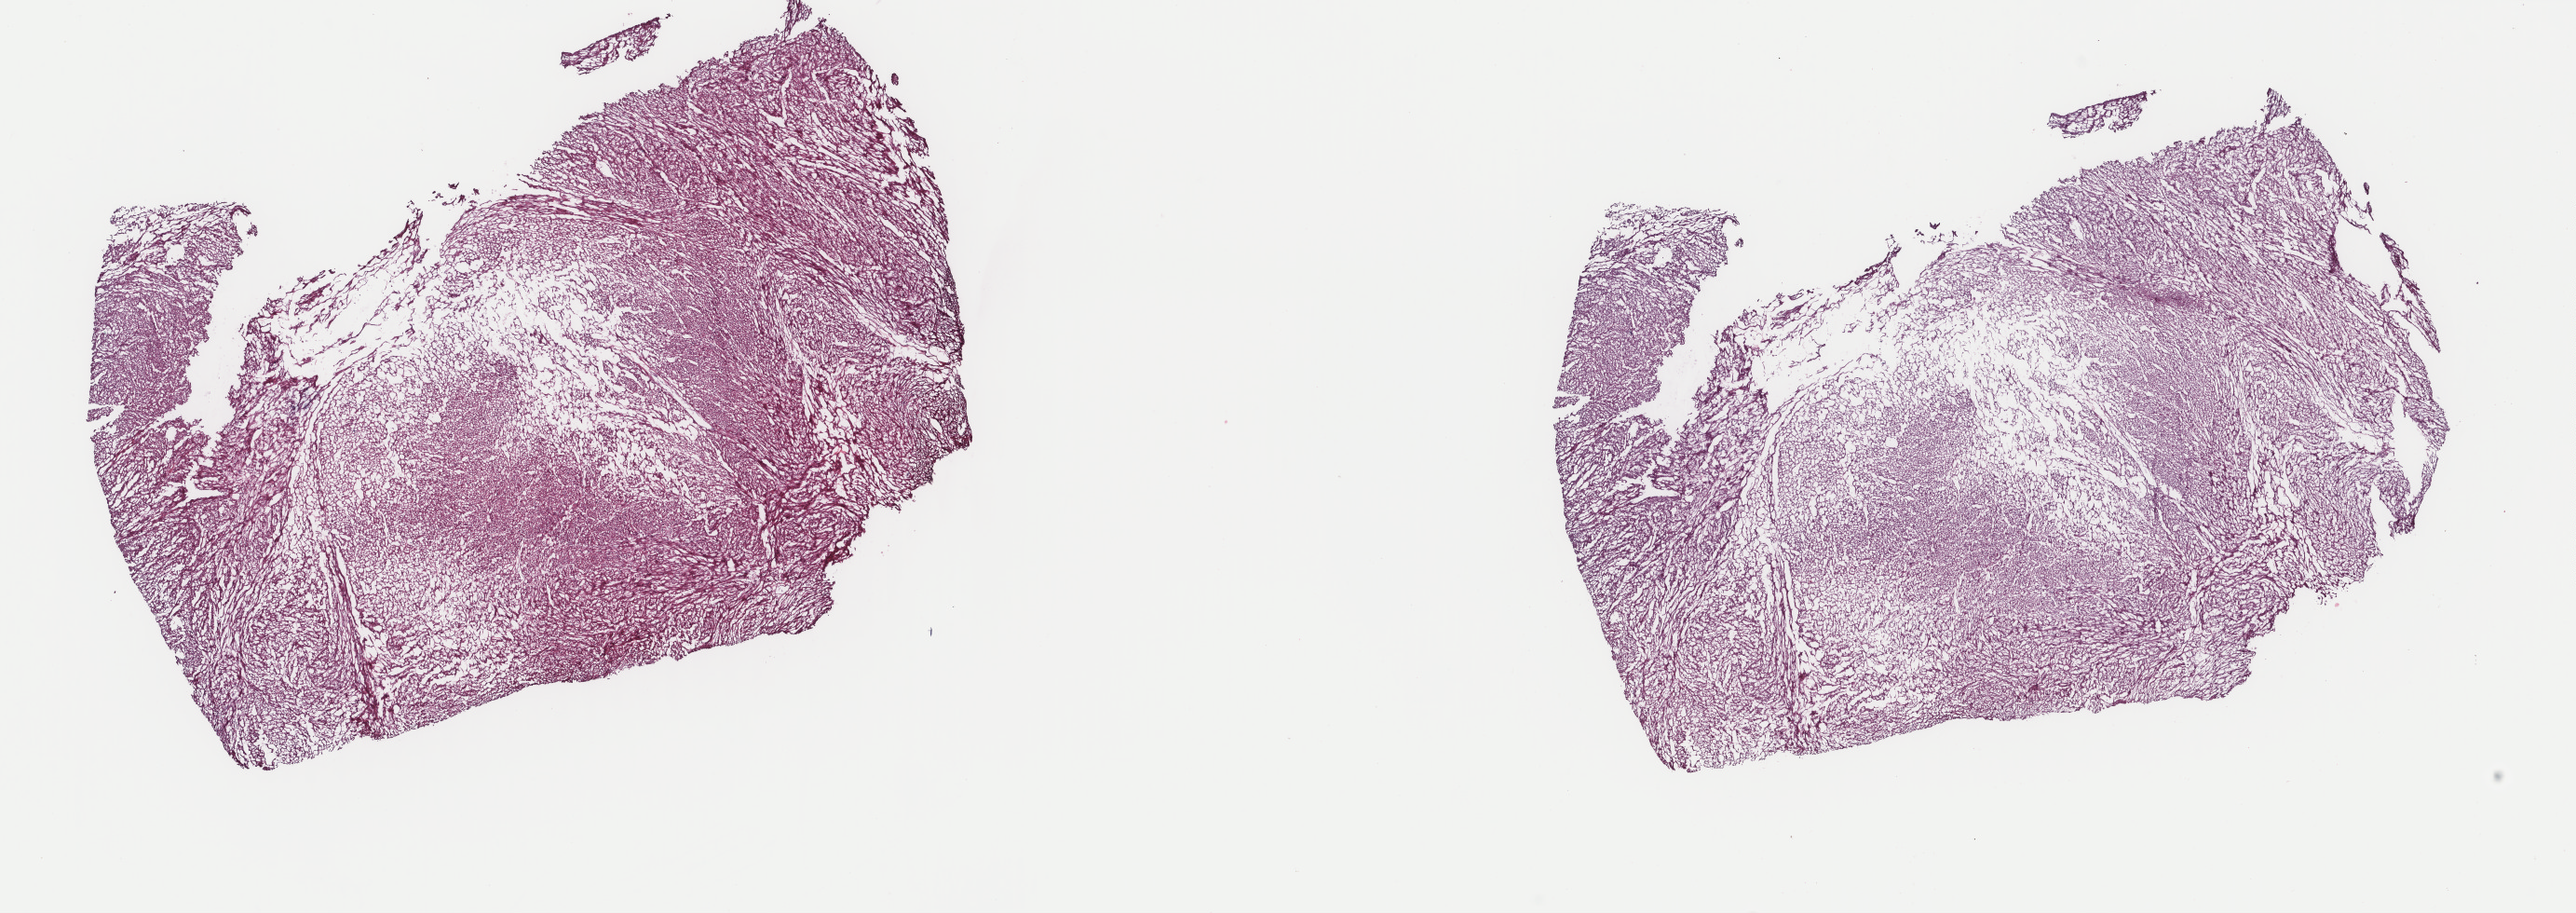
Whole-slide histology image, H&E-stained, a low-resolution overview of the entire scanned area, about 22.0 x 7.8 mm, frozen section from the top of the tissue portion, retroperitoneum and peritoneum, primary tumour sample. Patient: male, age at initial diagnosis 57 years. Slide review estimates, as recorded: tumour cells 80%, tumour nuclei 80%, normal cells 0%, stromal cells 20%, necrosis 0%. Inflammatory infiltration, as recorded: lymphocyte infiltration 1%, monocyte infiltration 1%, neutrophil infiltration 0%.
Pathologic diagnosis: Leiomyosarcoma, NOS (retroperitoneum).